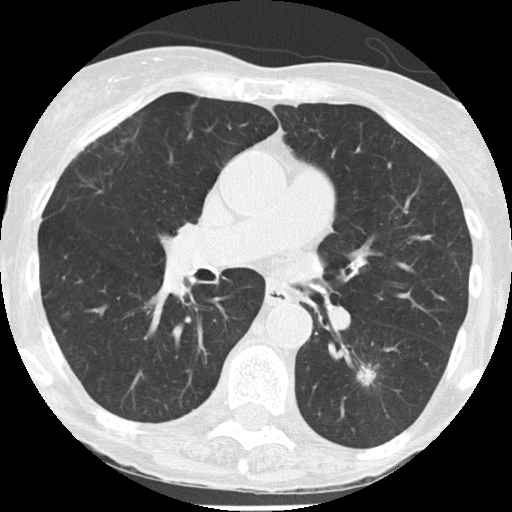
Low-dose screening chest CT, one axial slice. Slice 72 of 146 in the series (ordered by position). 120 kVp. Lung window (W 1500 / L -600 HU). 2 mm slice thickness. 512 × 512 image matrix, field of view 273 × 273 mm.
Outlined on this slice (expert manual segmentation):
- lesion 1 (tumor, lower lobe of left lung): box from (x=357, y=364) to (x=376, y=385) px